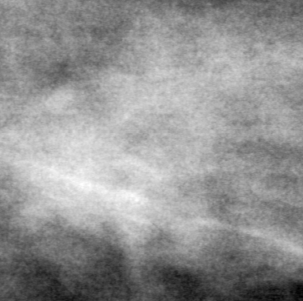
Crop from a digitized film mammogram around one marked abnormality; right breast; MLO view; BI-RADS breast density category 2 (scale 1–4).
Finding: mass, shape irregular, margins spiculated; BI-RADS assessment category 4; pathology (as recorded): malignant.